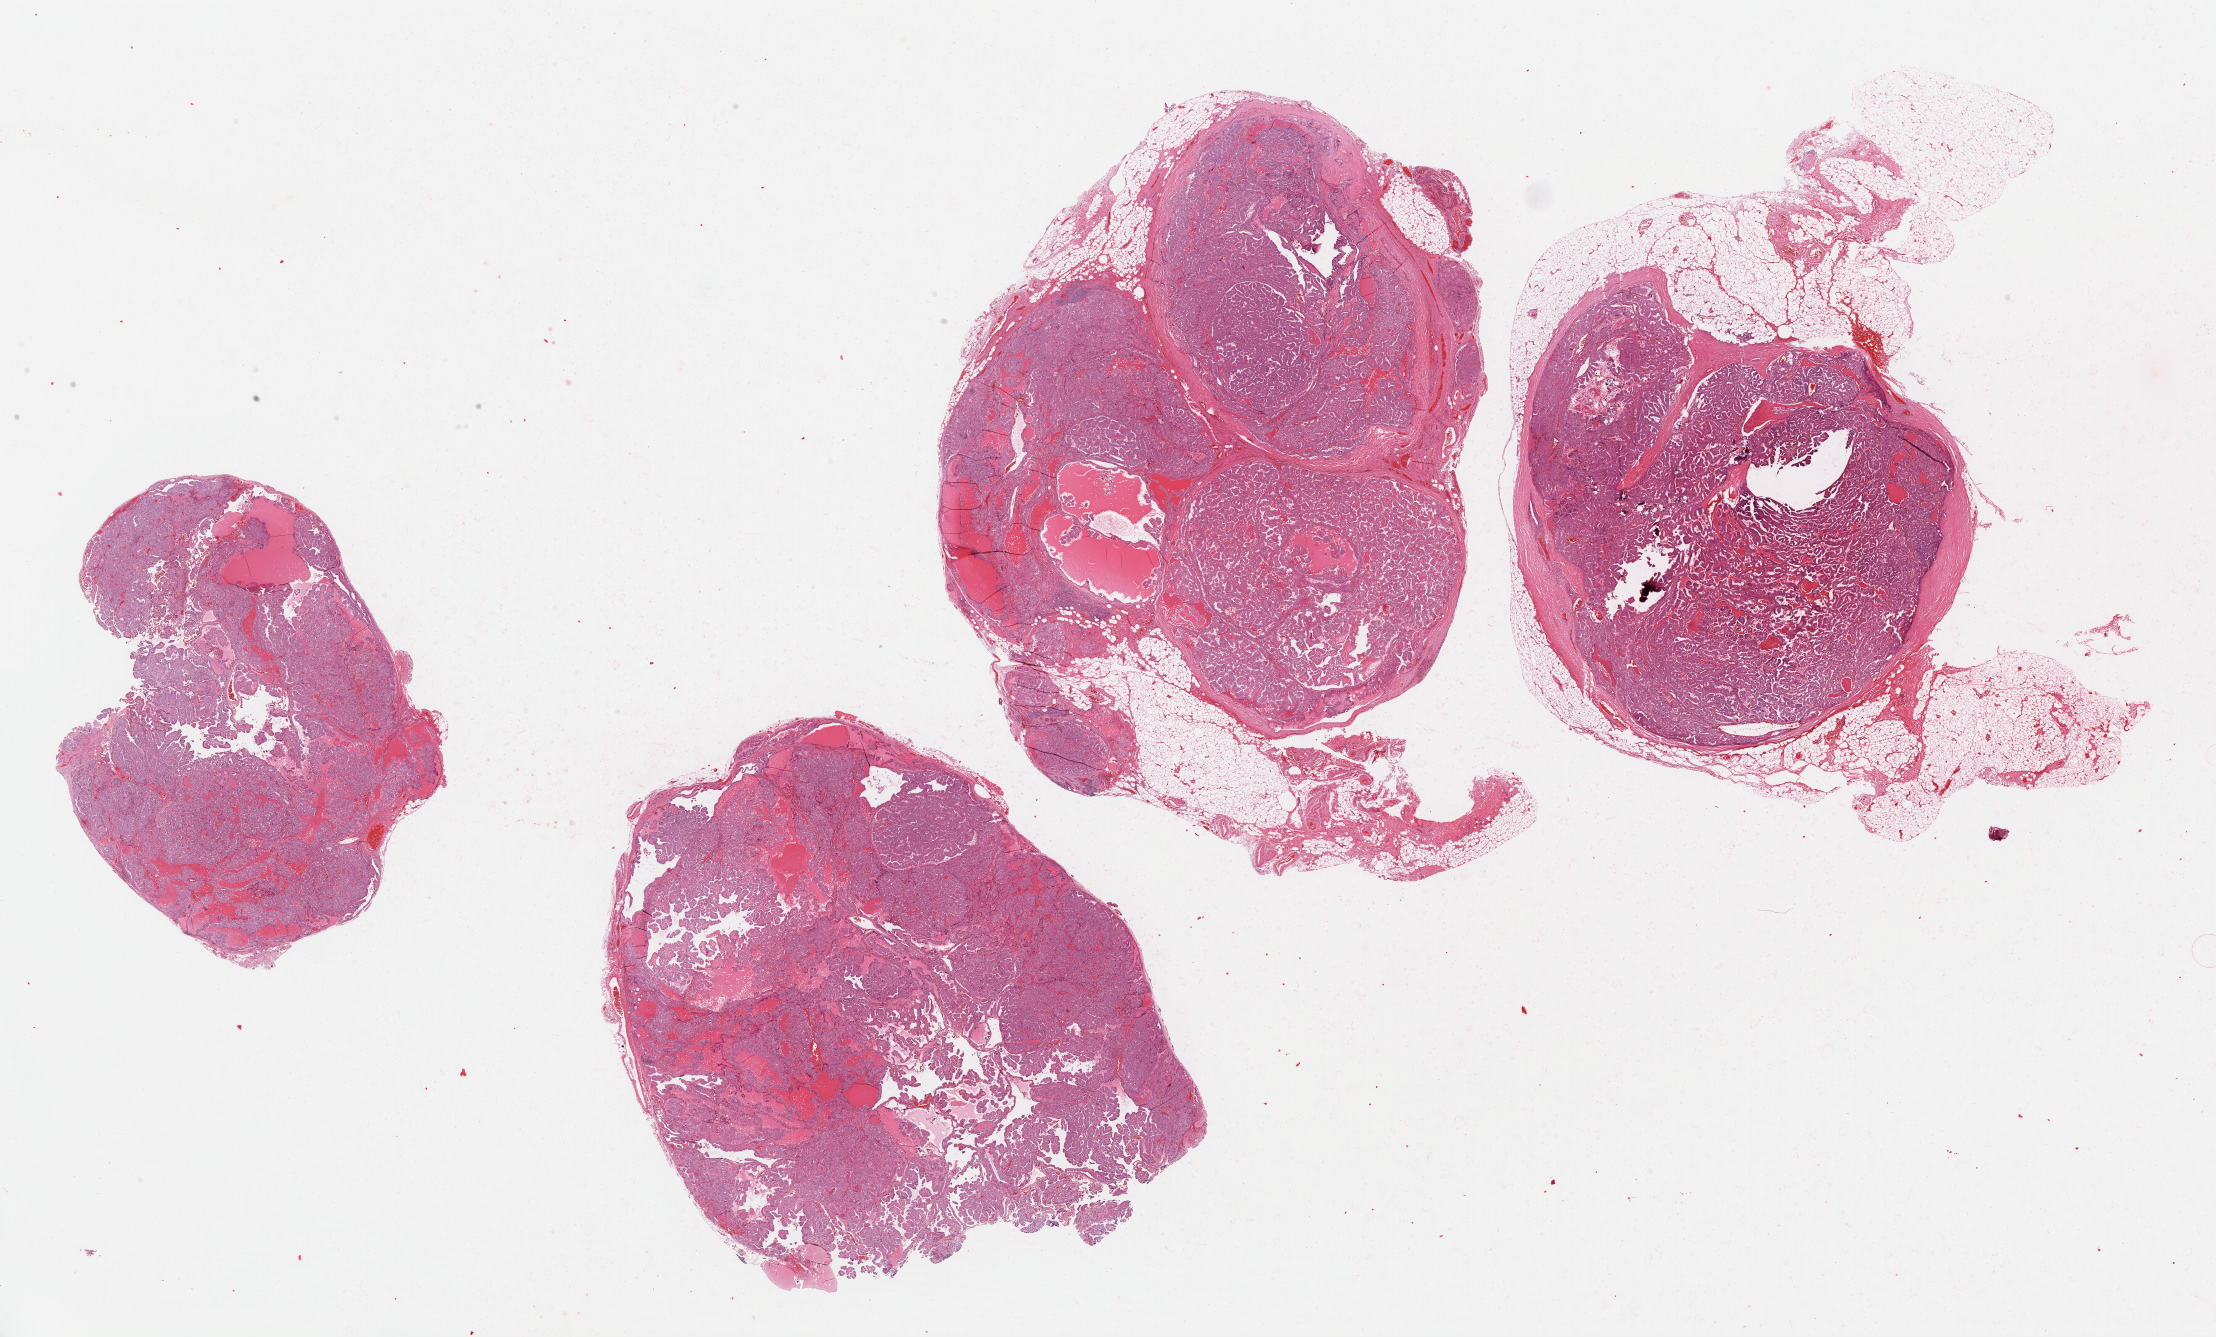
H&E-stained whole-slide image, low-resolution overview of the scanned area, about 35.0 x 21.1 mm (slide scanned at 40x); FFPE section; thyroid, primary tumour sample. Male patient; age at initial diagnosis 57 years.
Lymph nodes positive (case pathology): 13 of 28 examined. Laterality: bilateral. AJCC pathologic stage: IVA. Pathologic diagnosis: Papillary adenocarcinoma, NOS (thyroid gland). TNM: T4a N1b MX.